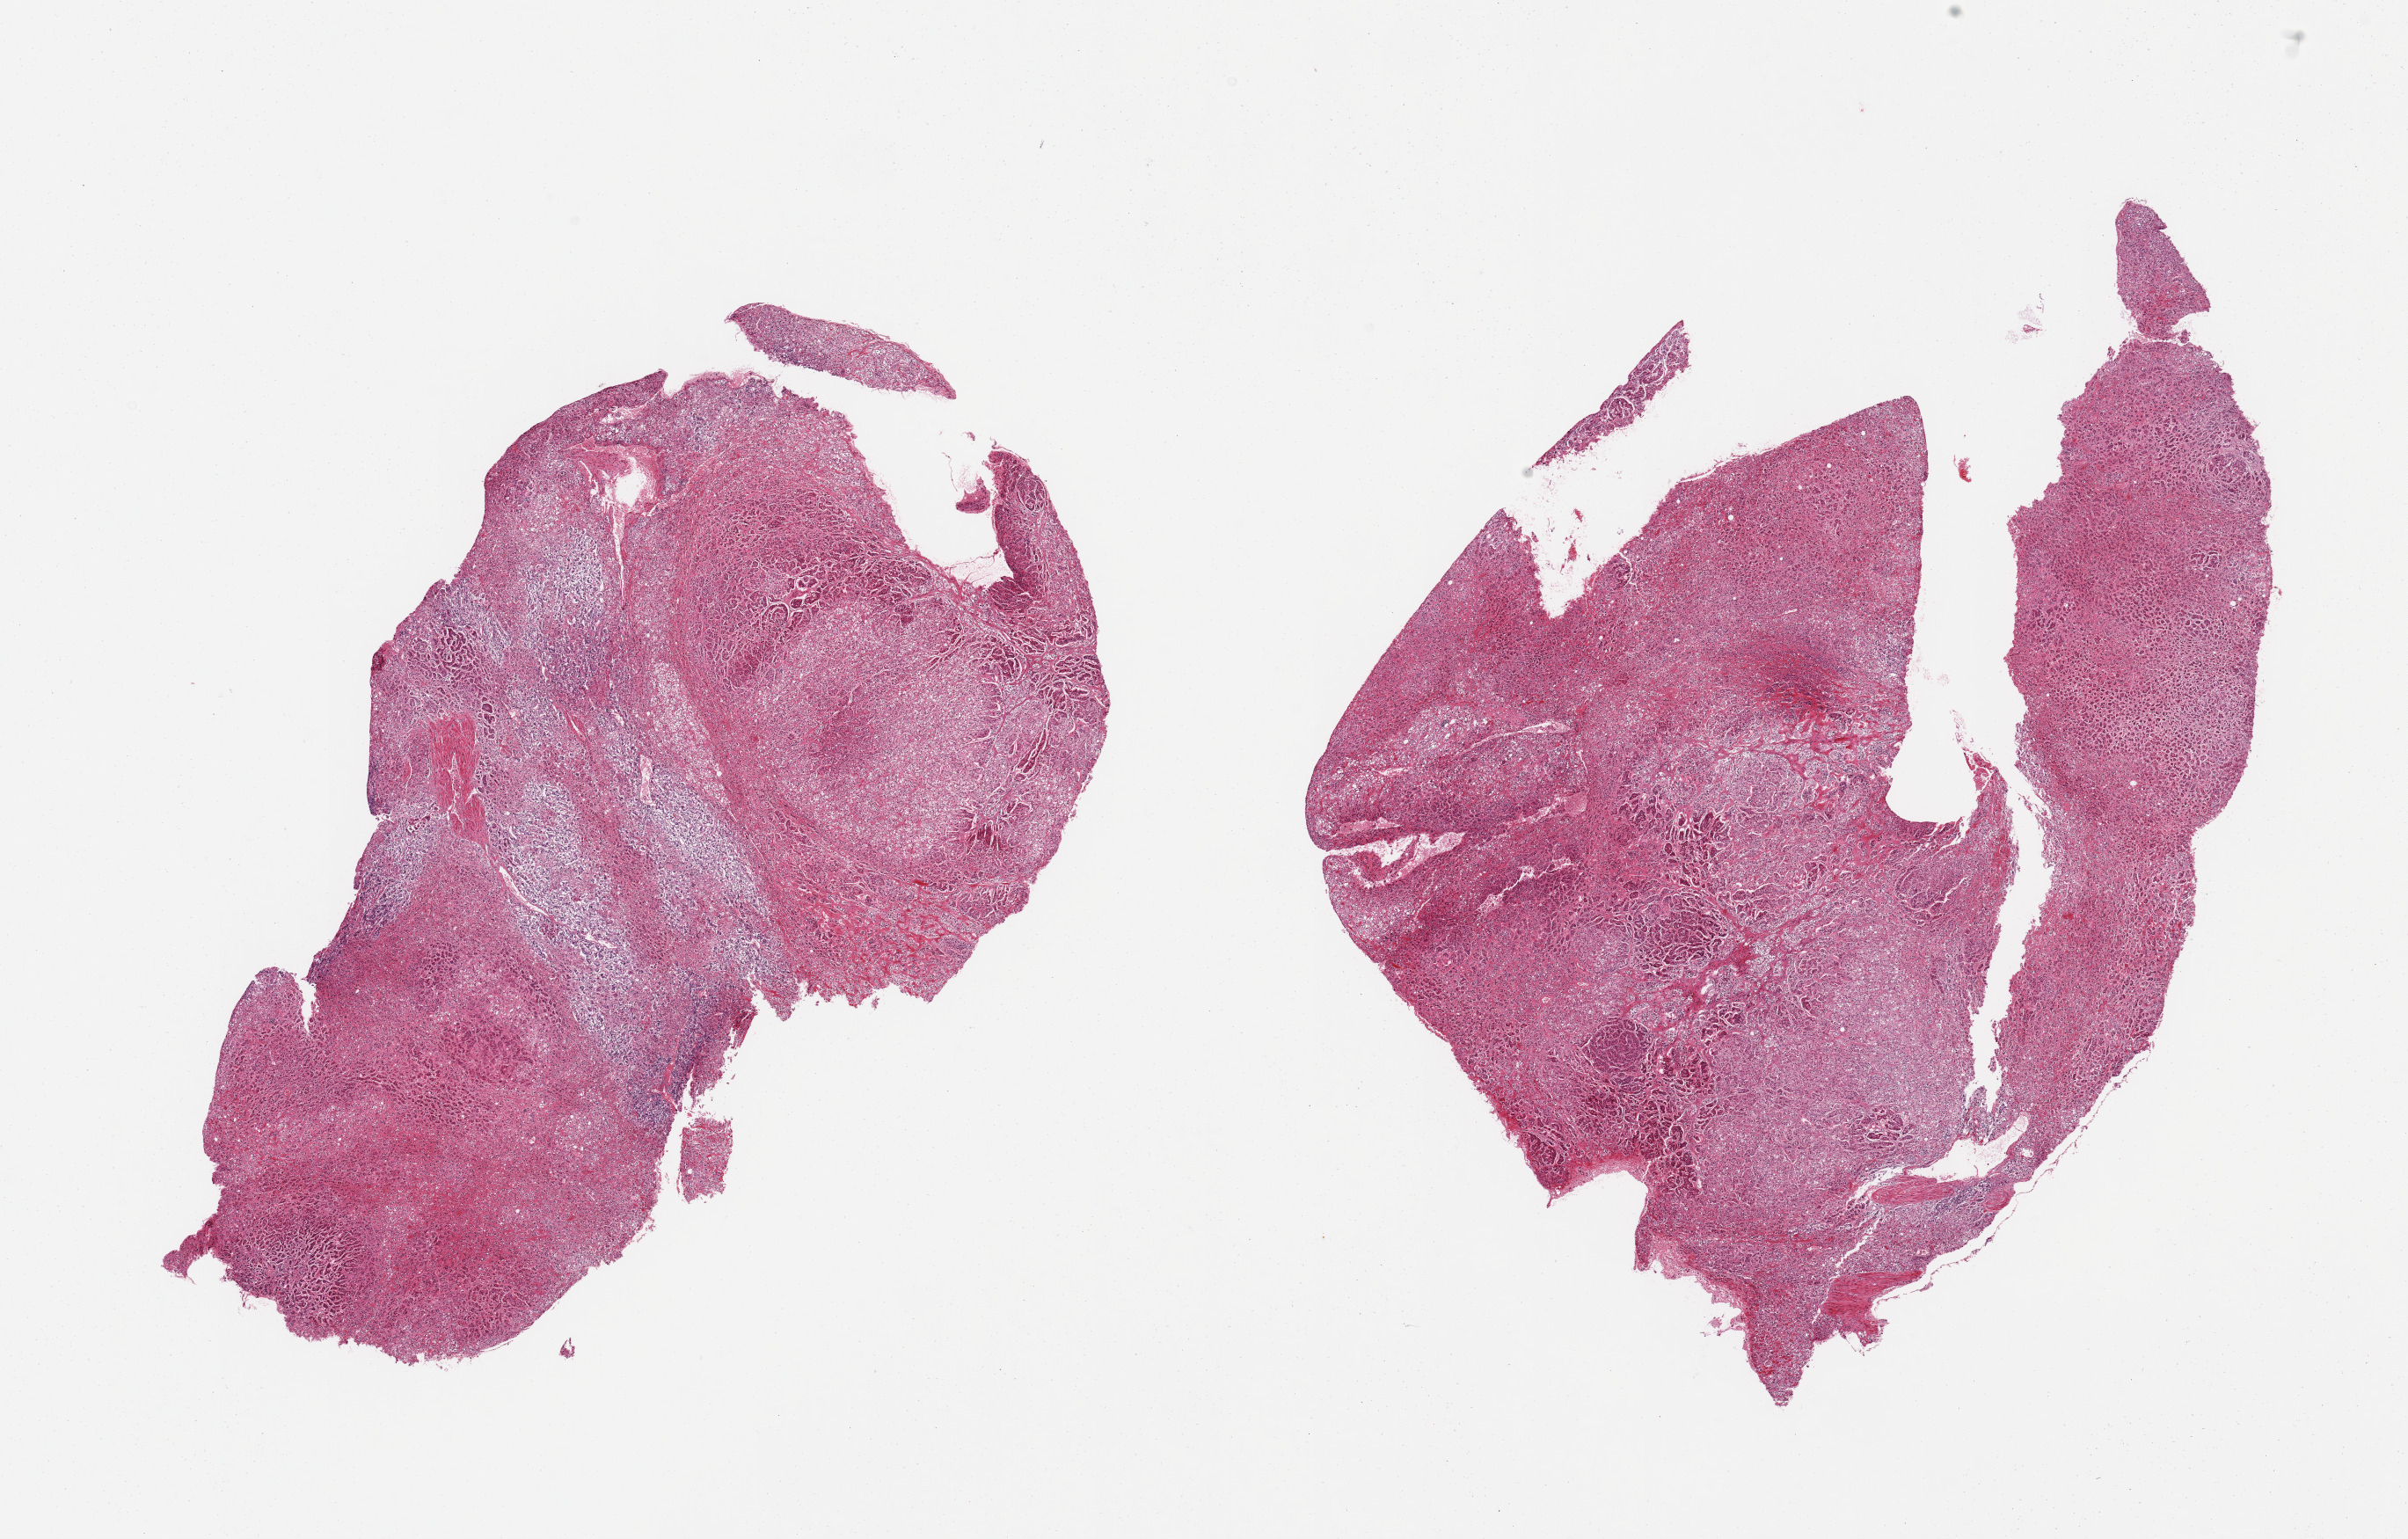
Haematoxylin and eosin whole-slide image, shown as a low-resolution overview of the whole scanned area (about 21.7 x 13.8 mm), PAXgene-fixed paraffin-embedded (PFPE) section, sampled site (target tissue): adrenal gland, donor tissue sample.
Pathologist's review note for this sample: 2 pieces; well trimmed, poorly preserved.